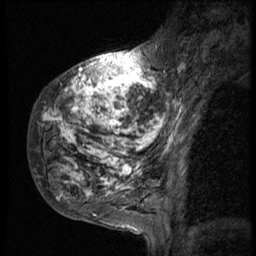
Breast MRI (dynamic contrast-enhanced), one sagittal slice. Slice 16 of 58 in the series (ordered by position). 3 images stored at this slice position (order not interpretable as contrast timing). 1.5 T. TE 4.2 ms, TR 9 ms. 256 × 256 image matrix, field of view 180 × 180 mm. Patient: female, 50 years. From the clinical record (not read from this slice): setting: breast cancer imaged before/during neoadjuvant chemotherapy; receptor status: triple-negative.
Annotated regions visible in this slice (semi-automatic segmentation, software-assisted and operator-edited):
- analysis volume of interest (the breast-tissue region the enhancement analysis was run in; not a lesion): box from (x=29, y=48) to (x=186, y=214) px
- tumour enhancement mask (voxels above the 140 % enhancement threshold inside the analysis volume of interest): (x=42, y=49)–(x=186, y=200)